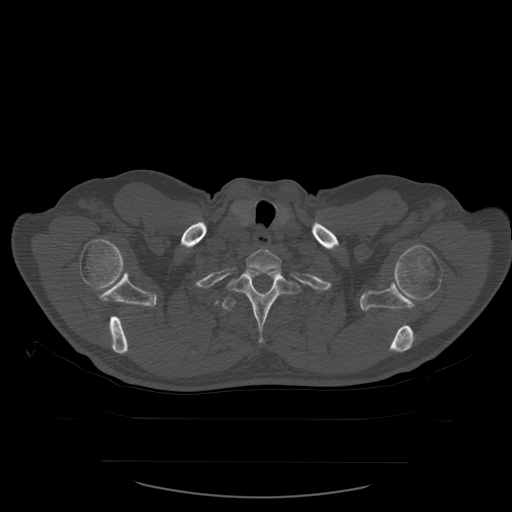
CT including the spine, one axial slice. Slice 476 of 590 in the series (ordered by position). Bone window (W 1800 / L 400 HU). 512 × 512 image matrix. Patient age 71 years. Case-level facts recorded for this patient, not image findings: primary cancer: lung; vertebrae with lytic lesions (as recorded): T1, T2, L5, S1.
Structures marked on this image (semi-automatically segmented with operator editing):
- T1 vertebra: bounding box [x1, y1, x2, y2] px = [247, 250, 282, 274]
- T2 vertebra: [225, 268, 304, 343]
- T3 vertebra: [222, 297, 238, 312]